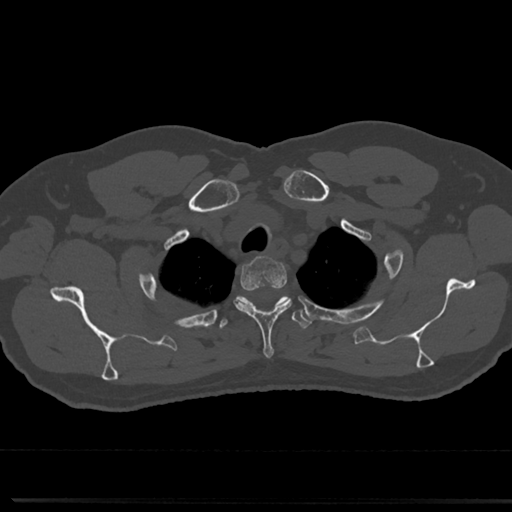
CT including the spine, one axial slice. Position 621 of 817 along the scan axis. Reconstruction kernel Br40s/3. 120 kVp. Bone window (W 1800 / L 400 HU). 0.5 mm slice thickness. 512 × 512 image matrix, field of view 355 × 355 mm. Patient: male, 61 years. From the clinical record (not read from this slice): primary cancer: prostate.
Structures marked on this image (semi-automatically segmented with operator editing):
- T2 vertebra: bounding box [x1, y1, x2, y2] px = [235, 260, 288, 353]
- T3 vertebra: [215, 294, 314, 333]